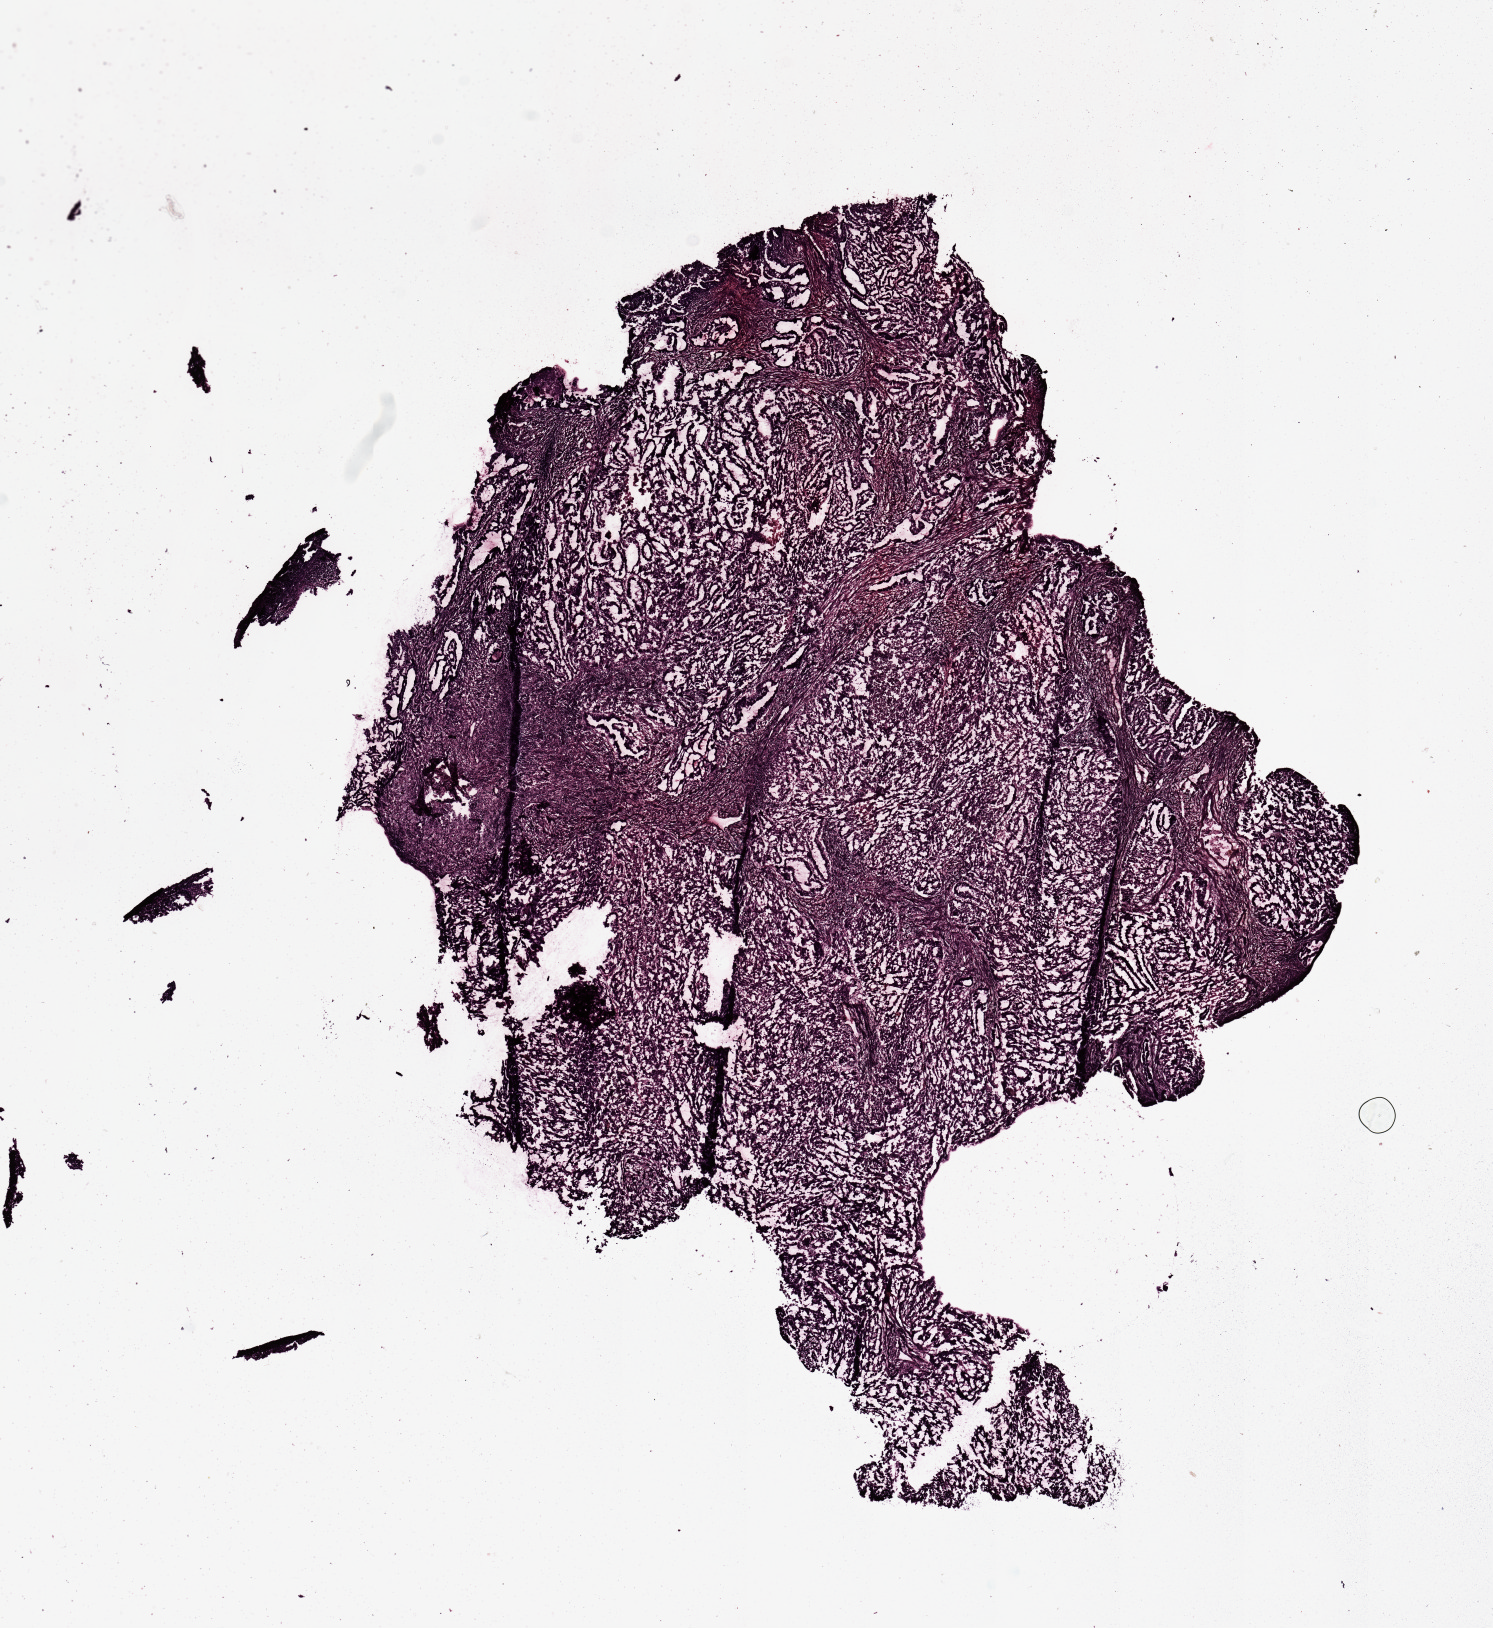
H&E whole-slide image — whole scanned area (about 11.8 x 12.9 mm) shown as a low-resolution overview; tumour tissue sample, uterus. Patient: female, age 78 years. Histologic grade: G2 (moderately differentiated).
* AJCC pathologic stage: I
* diagnosis: Endometrioid adenocarcinoma, NOS